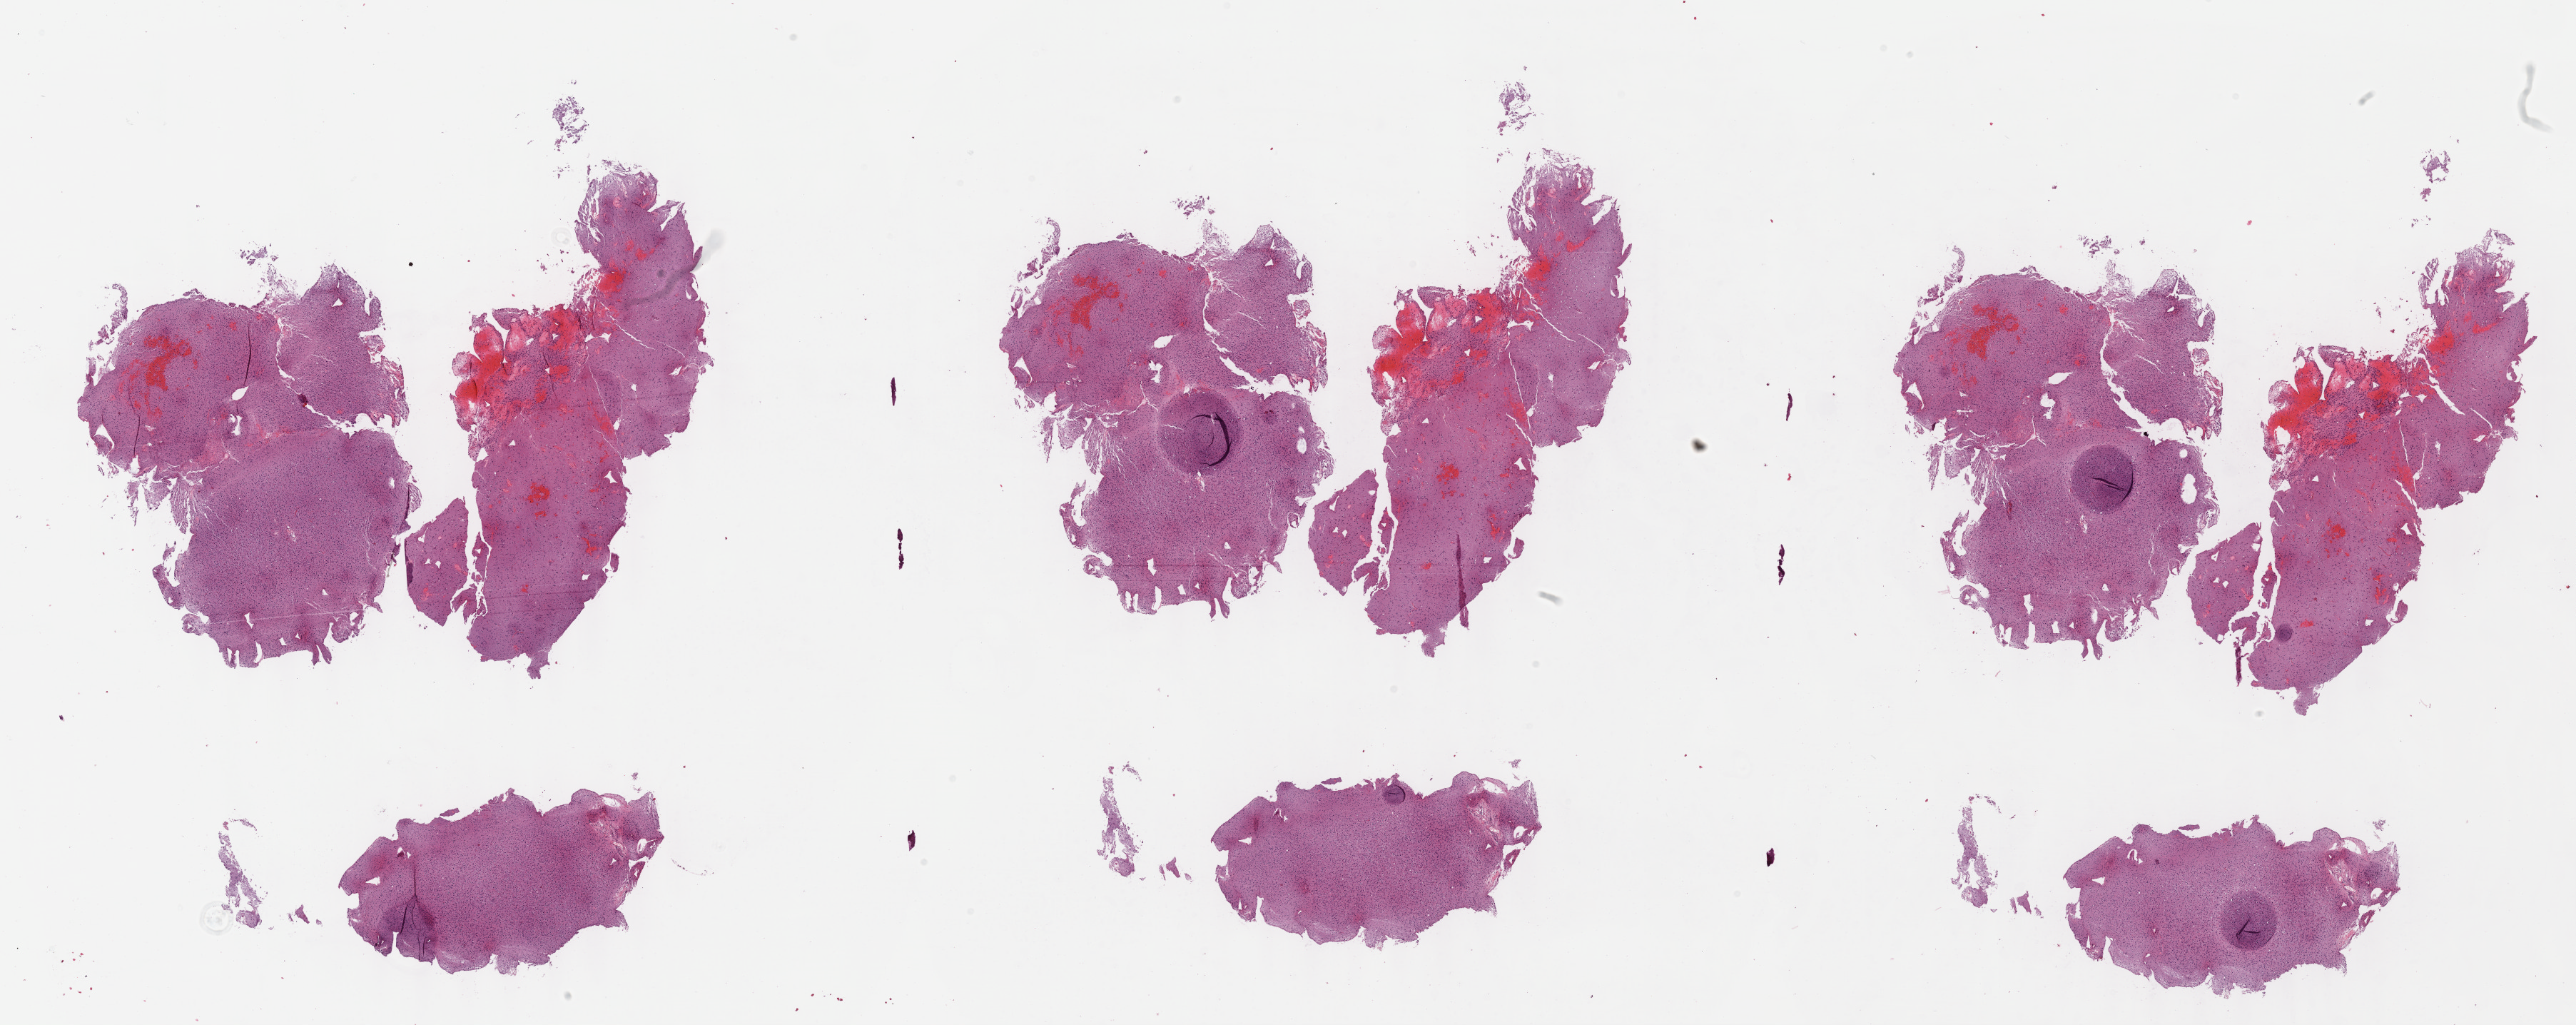
Digitized Hematoxylin and eosin (H&E) stained tissue section (whole slide), shown as a low-resolution overview of the whole scanned area (about 29.2 x 11.6 mm), formalin-fixed paraffin-embedded (FFPE) diagnostic section, sample: primary tumour, brain. Female patient; age at initial diagnosis 26 years. Histologic grade: G2 (moderately differentiated).
Diagnosis: Oligodendroglioma, NOS (cerebrum).